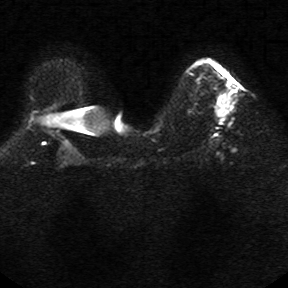
Breast MRI, one axial slice; position 18 of 34 along the scan axis; diffusion-weighted series; image 2 of 4 stored at this slice position (different b-values; order by instance number); 1.5 T; 5 mm slice thickness; 288 × 288 image matrix, field of view 340 × 340 mm. Female patient.
Outlined on this slice (expert manual segmentation):
- tumour on diffusion-weighted imaging: box from (x=222, y=99) to (x=232, y=115) px